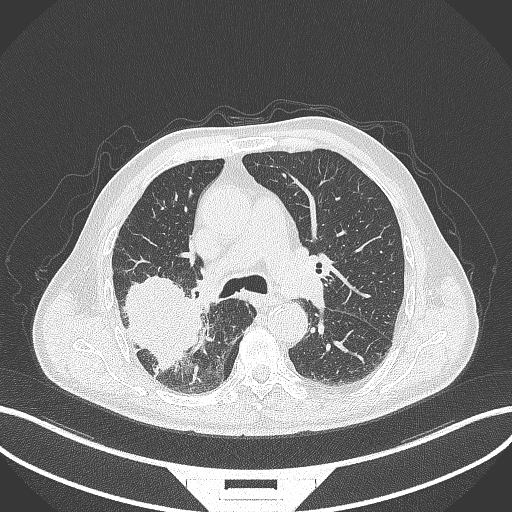
Chest CT, one axial slice. Slice 256 of 429 in the series (ordered by position). 120 kVp. Lung window (W 1500 / L -600 HU). 1 mm slice thickness. 512 × 512 image matrix, field of view 400 × 400 mm. Male patient, age 72 years. Case-level facts recorded for this patient, not image findings: clinical TNM (as recorded): T3 N2 M0.
Annotated regions visible in this slice (bounding box drawn by a radiologist):
- lung tumour (recorded histology: adenocarcinoma): bounding box <117,272,206,377> (left, top, right, bottom; pixels)